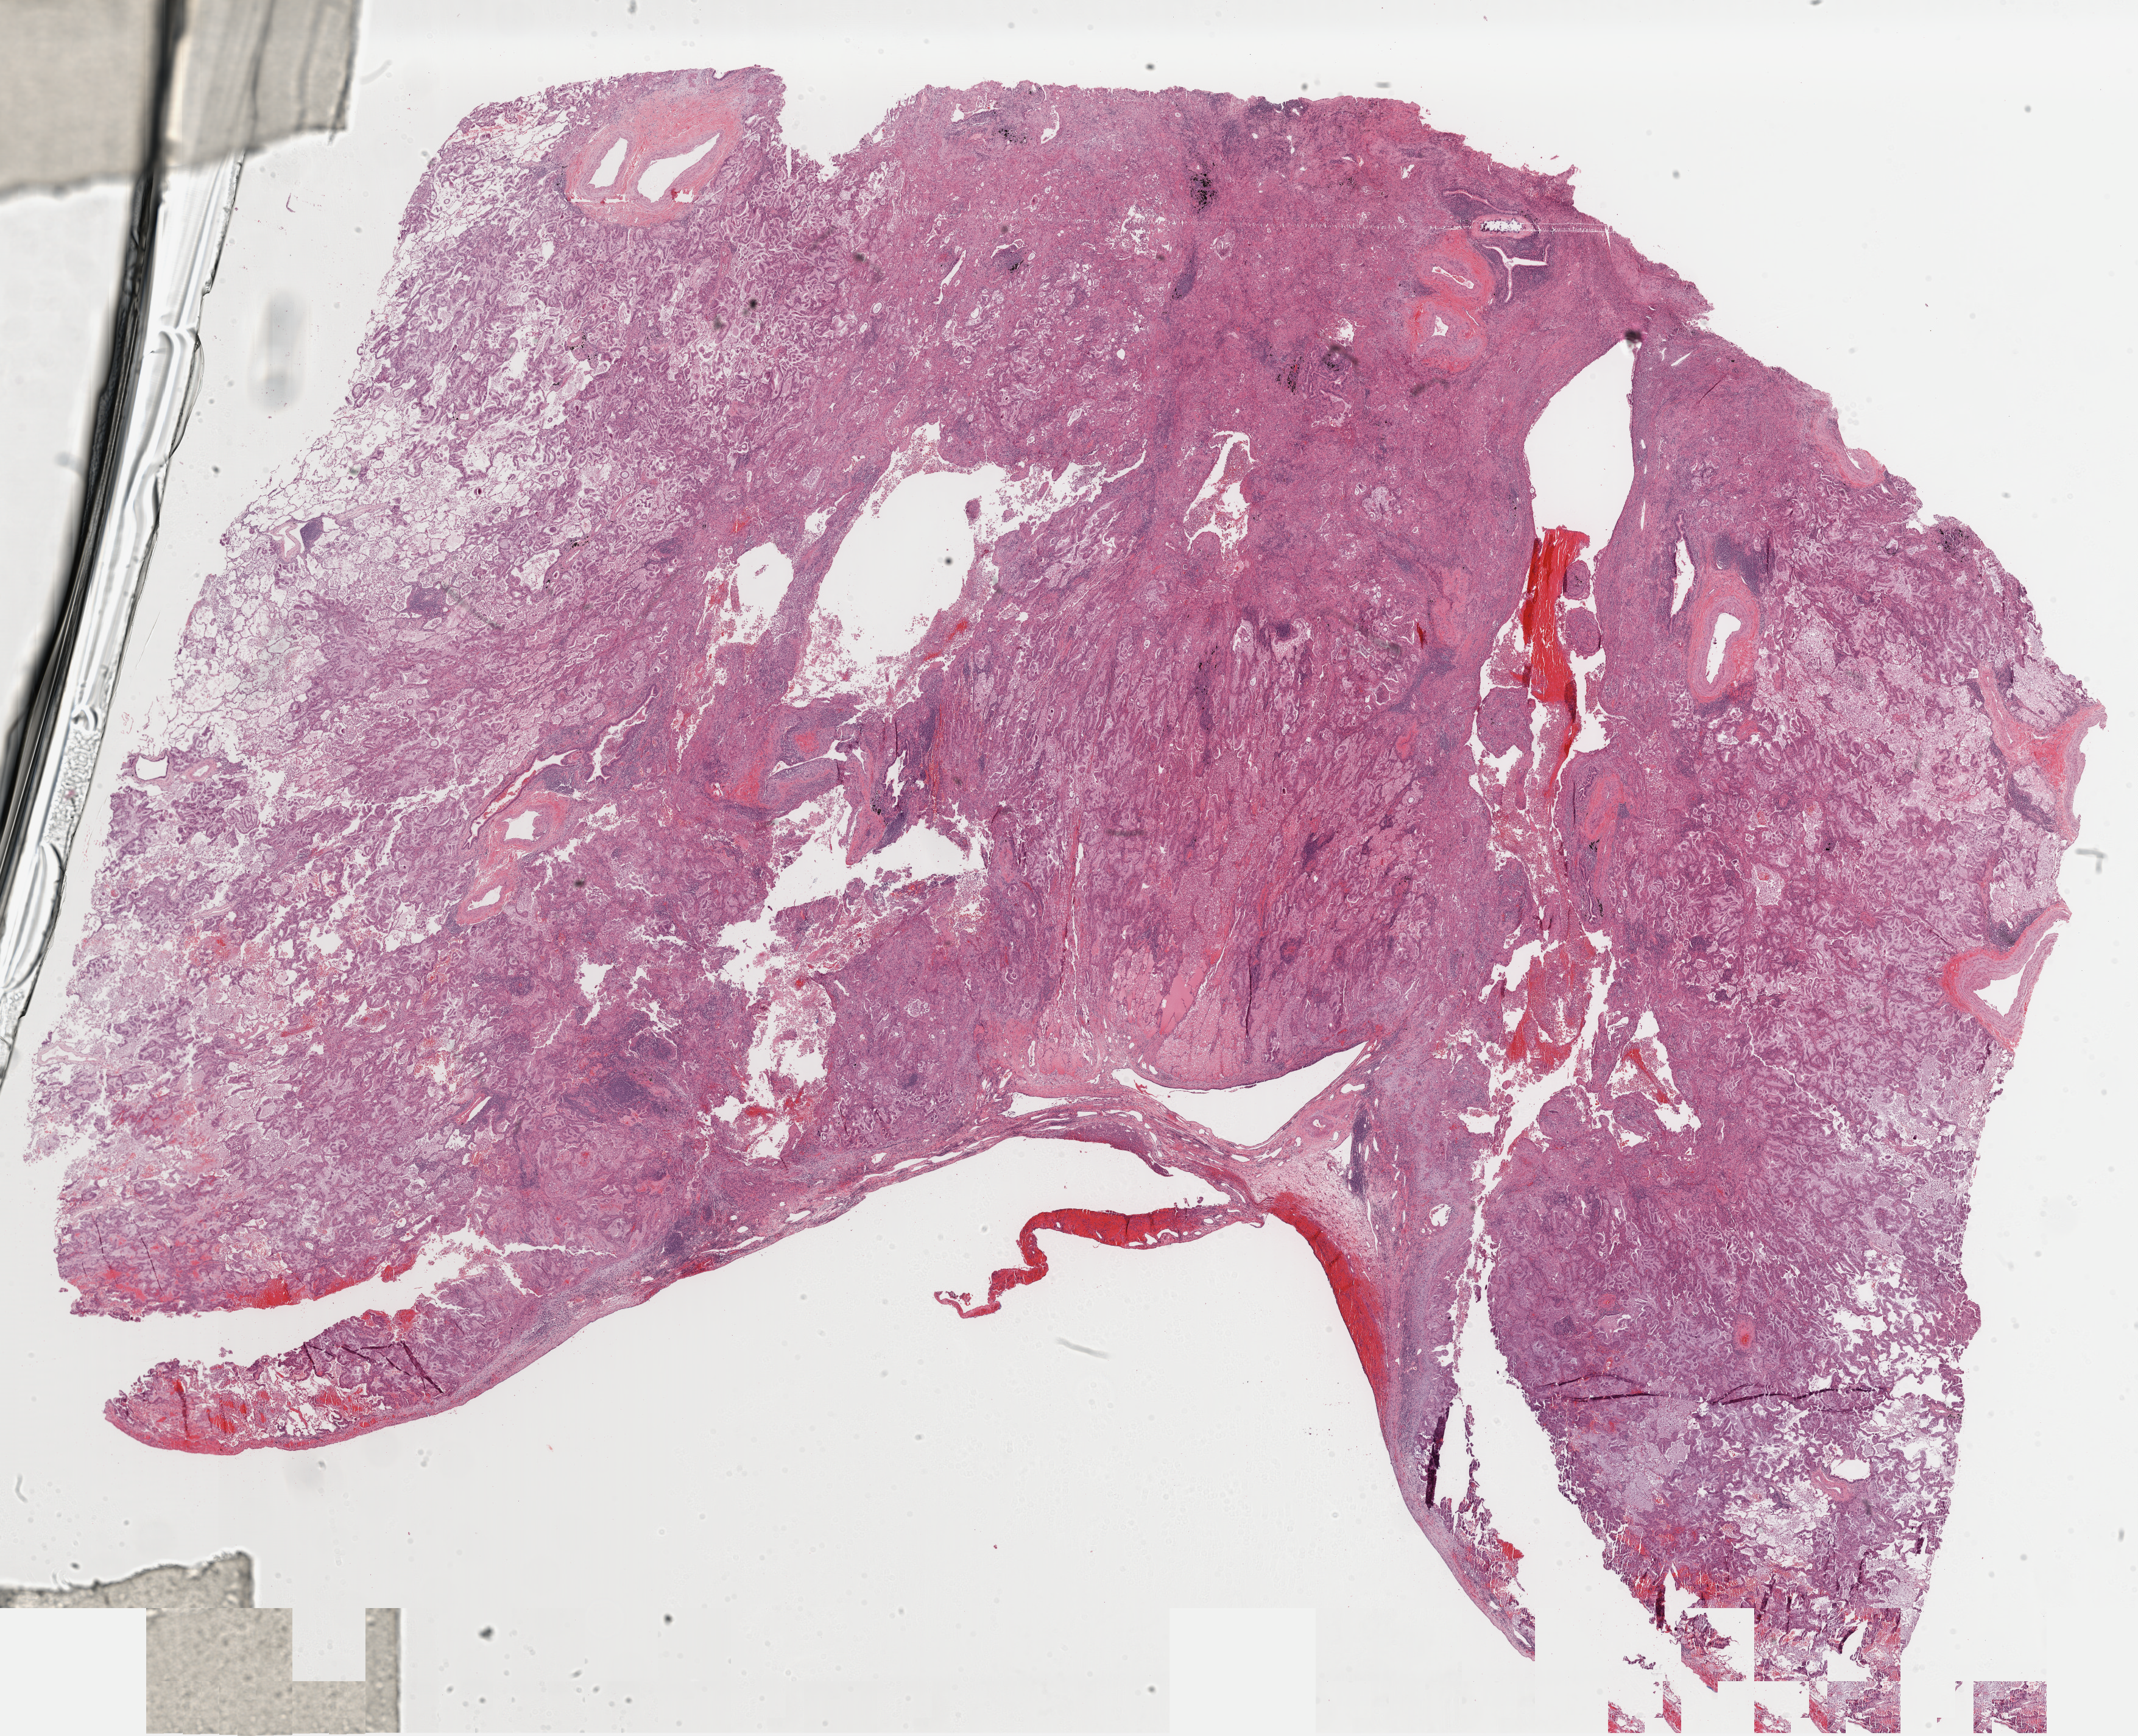
H&E-stained whole-slide image, a low-resolution overview of the entire scanned area, about 27.7 x 22.5 mm (acquisition: 40x scan), formalin-fixed paraffin-embedded (FFPE) diagnostic section, primary tumour sample from the lung. Male, age 68 years at initial diagnosis.
TNM: T3 N0 M0. AJCC pathologic stage: IIB (7th edition). Histologic diagnosis: Mucinous adenocarcinoma (lower lobe, lung).